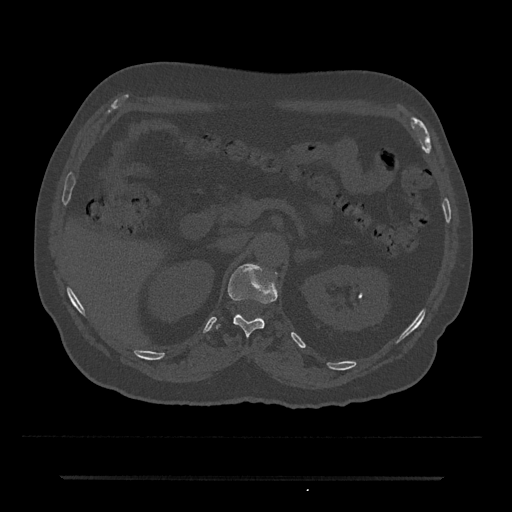
CT including the spine, one axial slice; slice 120 of 797 in the series (ordered by position); 120 kVp; bone window (W 1800 / L 400 HU); 0.5 mm slice thickness; 512 × 512 image matrix, field of view 437 × 437 mm. Patient: male, 69 years. Case-level facts recorded for this patient, not image findings: primary cancer: prostate.
Structures marked on this image (semi-automatic segmentation, software-assisted and operator-edited):
- T12 vertebra: bounding box [x1, y1, x2, y2] px = [216, 264, 278, 336]